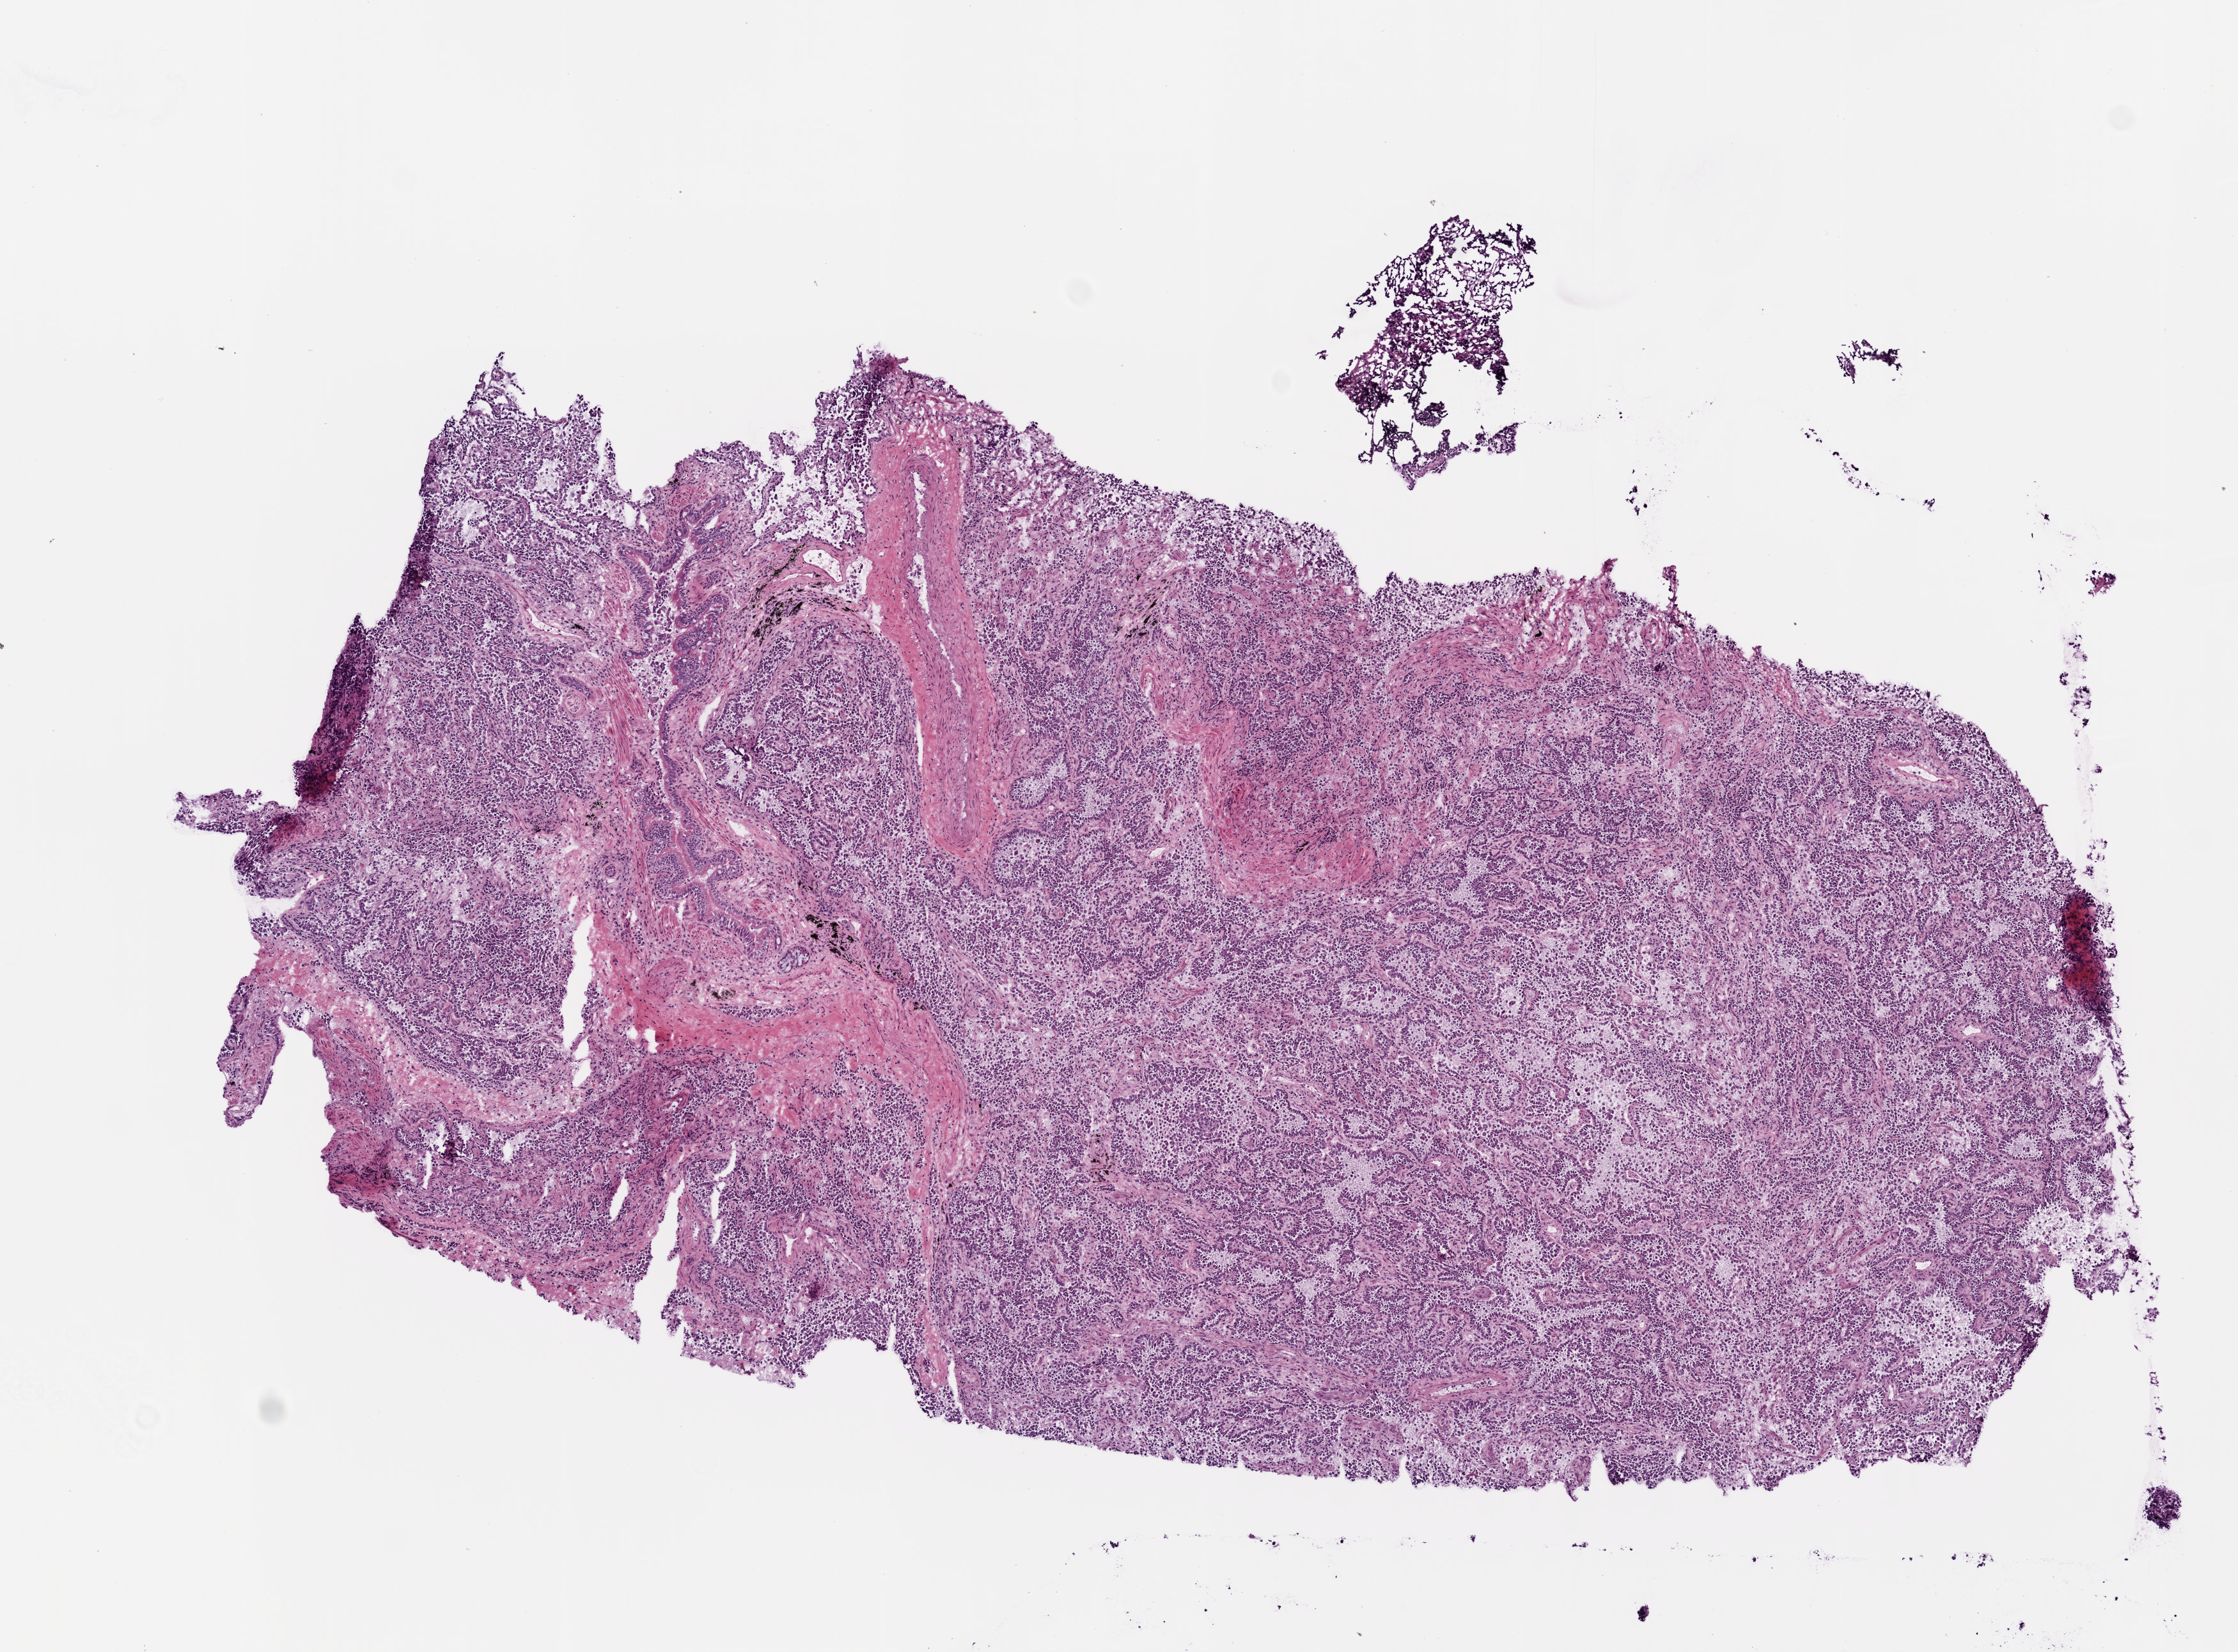
H&E whole-slide image — whole scanned area (about 7.0 x 5.2 mm) shown as a low-resolution overview, frozen section, primary tumour sample from the lung. Male patient; age at initial diagnosis 68 years. Pathologist review of this section (percent, as recorded): tumour cells 80%, tumour nuclei 75%, normal cells 5%, stromal cells 15%, necrosis 0%.
- histologic diagnosis: Adenocarcinoma, NOS